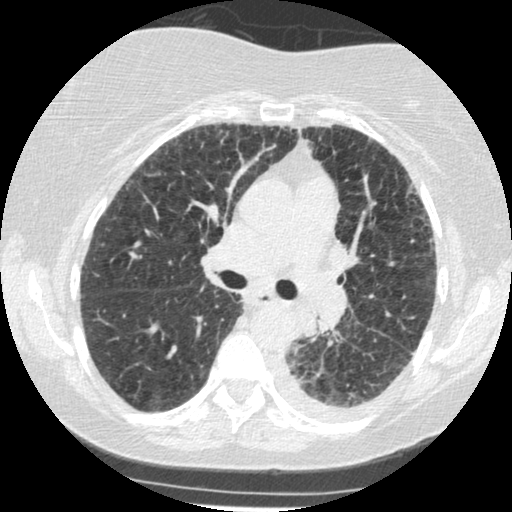
Low-dose screening chest CT, one axial slice. Slice 162 of 341 in the series (ordered by position). 120 kVp. Lung window (W 1500 / L -600 HU). 1.25 mm slice thickness. 512 × 512 image matrix.
Annotated regions visible in this slice (expert manual segmentation):
- lesion 1 (tumor, lower lobe of left lung): bounding box [x1, y1, x2, y2] px = [294, 307, 317, 336]